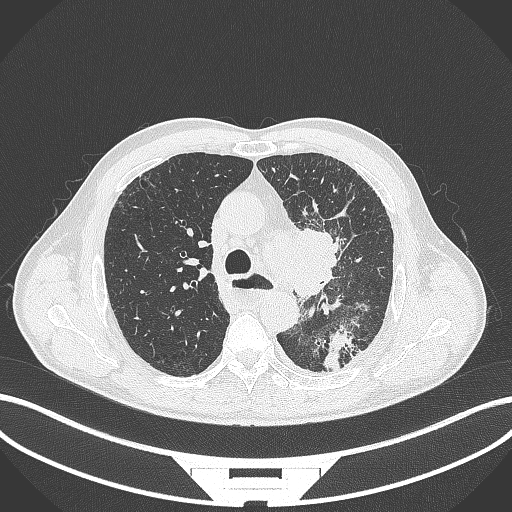
Chest CT, one axial slice; slice 265 of 411 in the series (ordered by position); reconstruction kernel B70f; 120 kVp; lung window (W 1500 / L -600 HU); 1 mm slice thickness; 512 × 512 image matrix, field of view 400 × 400 mm. Patient: male, 57 years. Case-level facts recorded for this patient, not image findings: clinical TNM (as recorded): T2a N1 M0.
Outlined on this slice (rectangle marked by the reading radiologist):
- lung tumour (recorded histology: squamous cell carcinoma): bounding box [x1, y1, x2, y2] px = [290, 225, 355, 307]